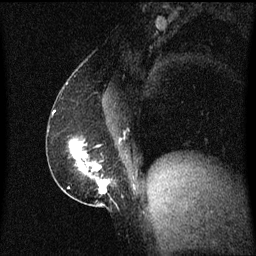
Breast MRI (dynamic contrast-enhanced), one sagittal slice. Slice 30 of 60 in the series (ordered by position). Dynamic contrast-enhanced series, image 2 of 3 at this slice position (ordered by acquisition). 1.5 T. TE 4.2 ms, TR 8.4 ms. 2 mm slice thickness. 256 × 256 image matrix, field of view 200 × 200 mm. Patient: female, 52 years. From the clinical record (not read from this slice): setting: breast cancer imaged before/during neoadjuvant chemotherapy; receptor status: HER2-positive.
Structures marked on this image (semi-automatic segmentation, software-assisted and operator-edited):
- analysis volume of interest (the breast-tissue region the enhancement analysis was run in; not a lesion): bounding box <62,136,116,203> (left, top, right, bottom; pixels)
- tumour enhancement mask (voxels above the 70 % enhancement threshold inside the analysis volume of interest): <70,140,109,195>